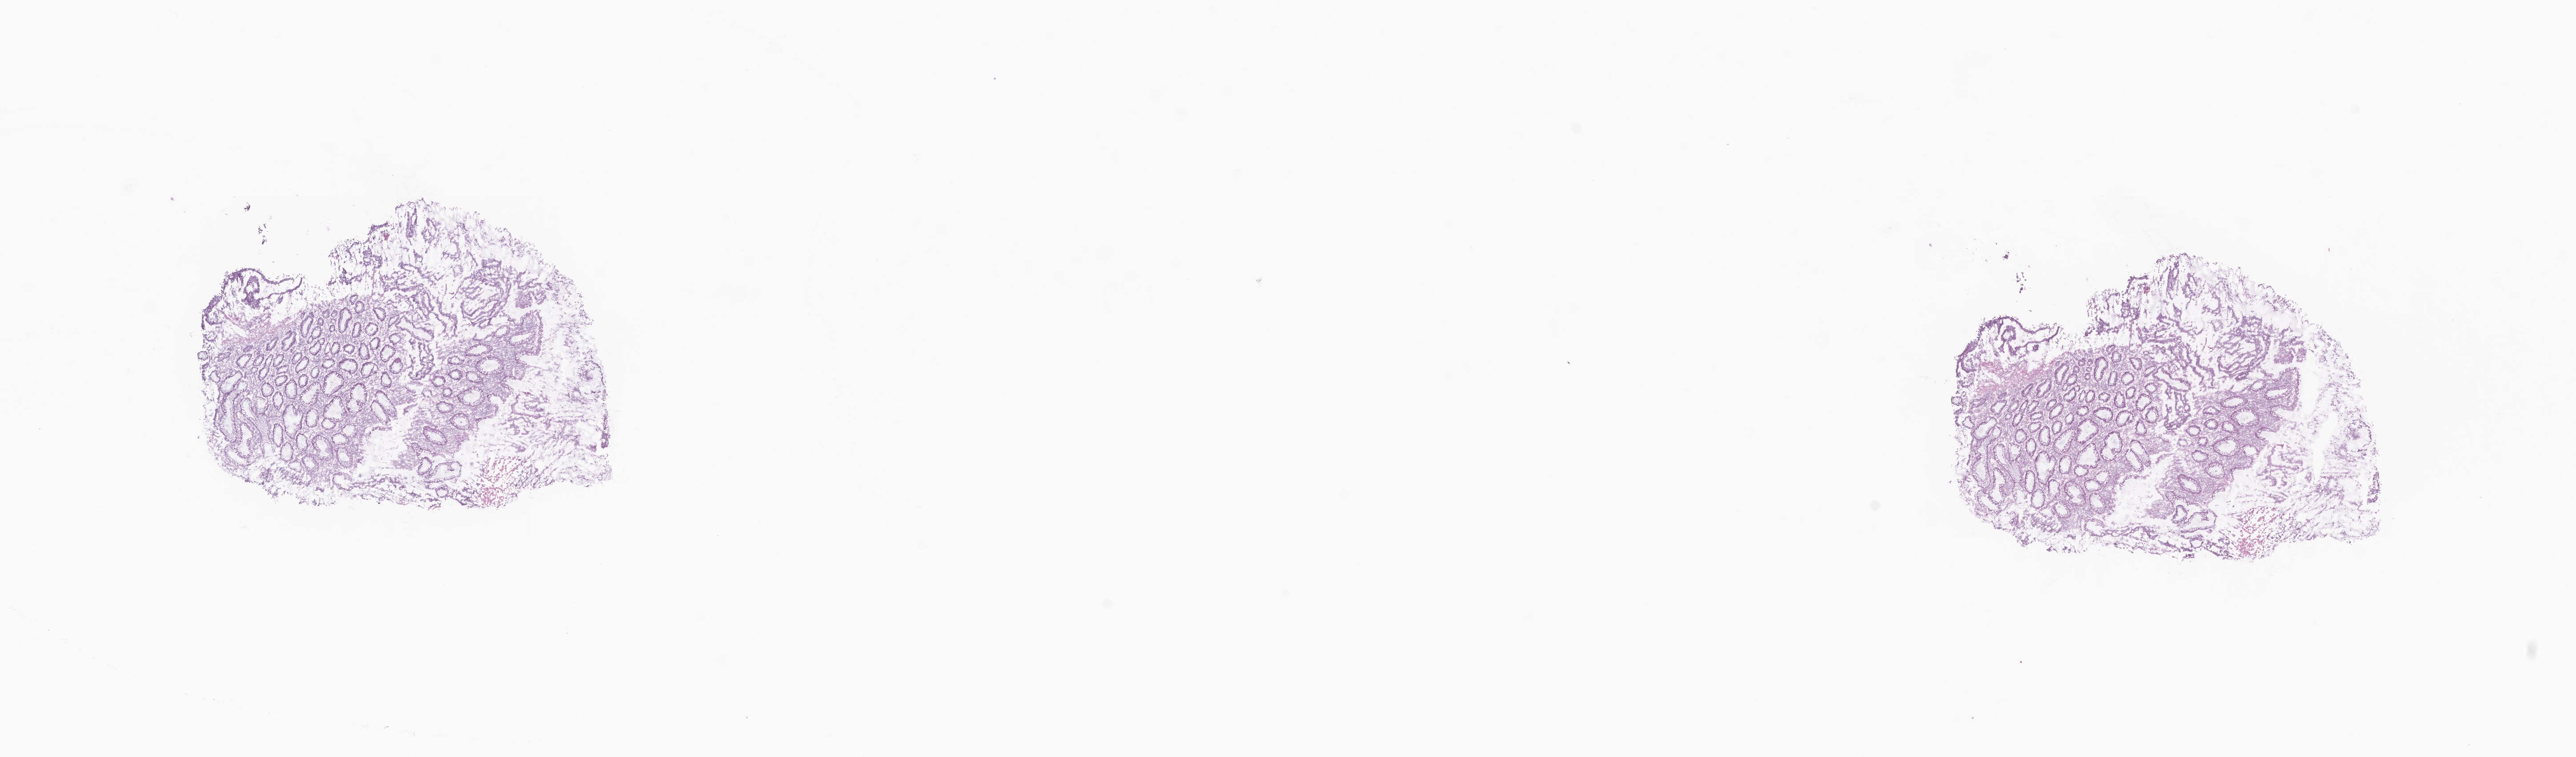
Digitized hematoxylin and eosin (H&E)-stained section — shown as a low-resolution overview of the whole scanned area (about 24.4 x 7.2 mm), cryosection, specimen: primary tumor, site: sigmoid colon. Male patient; age at initial diagnosis 69 years. Slide review estimates, as recorded: tumor cells 50%, tumor nuclei 50%, stromal cells 15%, necrosis 0%, normal cells 35%. Inflammatory infiltration, as recorded: lymphocyte infiltration 4%, monocyte infiltration 2%, neutrophil infiltration 5%.
* section: top of the tissue portion
* histologic diagnosis: Adenocarcinoma, NOS